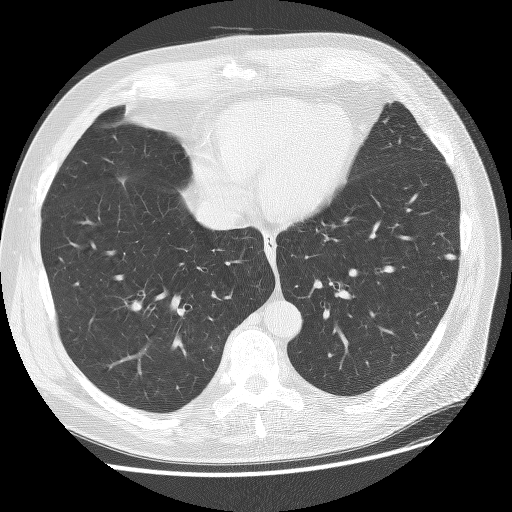
Low-dose screening chest CT, one axial slice. 120 kVp. Lung window (W 1500 / L -600 HU). 2.5 mm slice thickness. 512 × 512 image matrix, field of view 380 × 380 mm.
Outlined on this slice (expert manual segmentation):
- lesion 4 (tumor): bounding box [x1, y1, x2, y2] px = [446, 254, 455, 260]